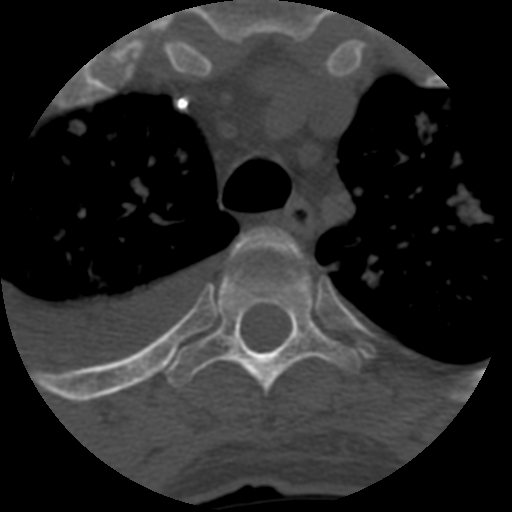
CT including the spine, one axial slice. Position 475 of 708 along the scan axis. Reconstruction kernel STANDARD. 120 kVp. One of 3 acquisitions stored at this slice position. Bone window (W 1800 / L 400 HU). 512 × 512 image matrix, field of view 160 × 160 mm. Patient age 55 years. Case-level facts recorded for this patient, not image findings: primary cancer: colon.
Outlined on this slice (semi-automatic segmentation, software-assisted and operator-edited):
- T3 vertebra: bounding box (x1, y1, x2, y2) in pixels: (238, 227, 297, 252)
- T4 vertebra: (165, 247, 362, 396)